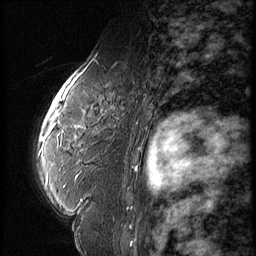
Breast MRI (dynamic contrast-enhanced), one sagittal slice. Position 39 of 56 along the scan axis. Dynamic contrast-enhanced series, image 2 of 3 at this slice position (ordered by acquisition). 1.5 T. TE 4.2 ms, TR 9 ms. 2.5 mm slice thickness. 256 × 256 image matrix, field of view 180 × 180 mm. Patient: female, 59 years. Case-level facts recorded for this patient, not image findings: setting: breast cancer imaged before/during neoadjuvant chemotherapy; receptor status: HER2-positive.
Annotated regions visible in this slice (semi-automatically segmented with operator editing):
- analysis volume of interest (the breast-tissue region the enhancement analysis was run in; not a lesion): bounding box (x1, y1, x2, y2) in pixels: (44, 66, 151, 135)
- tumour enhancement mask (voxels above the 140 % enhancement threshold inside the analysis volume of interest): (46, 83, 68, 135)